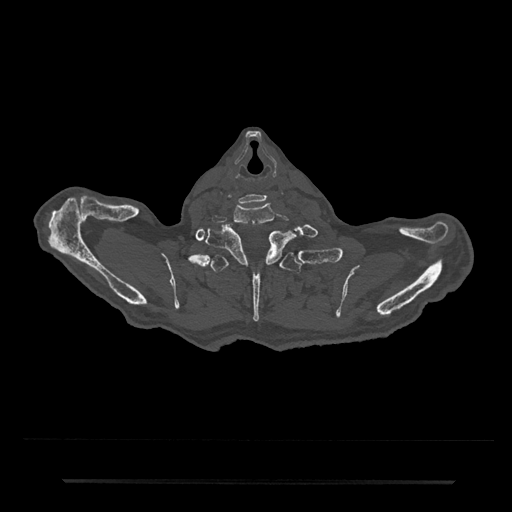
CT including the spine, one axial slice. Position 716 of 797 along the scan axis. 120 kVp. Bone window (W 1800 / L 400 HU). 0.5 mm slice thickness. 512 × 512 image matrix, field of view 427 × 427 mm. Patient: male, 74 years. Case-level facts recorded for this patient, not image findings: primary cancer: prostate.
Outlined on this slice (semi-automatically segmented with operator editing):
- T1 vertebra: bounding box <206,225,295,265> (left, top, right, bottom; pixels)
- T2 vertebra: <200,253,313,322>